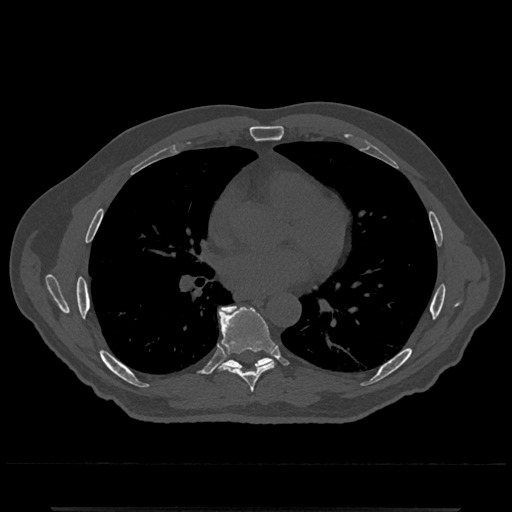
CT including the spine, one axial slice. Position 704 of 797 along the scan axis. Reconstruction kernel Br40s/3. Bone window (W 1800 / L 400 HU). 0.5 mm slice thickness. 512 × 512 image matrix, field of view 393 × 393 mm. Patient: male, 67 years. Case-level facts recorded for this patient, not image findings: primary cancer: prostate.
Annotated regions visible in this slice (semi-automatic segmentation, software-assisted and operator-edited):
- T7 vertebra: box from (x=219, y=307) to (x=276, y=393) px
- T8 vertebra: (x=219, y=305)–(x=271, y=370)